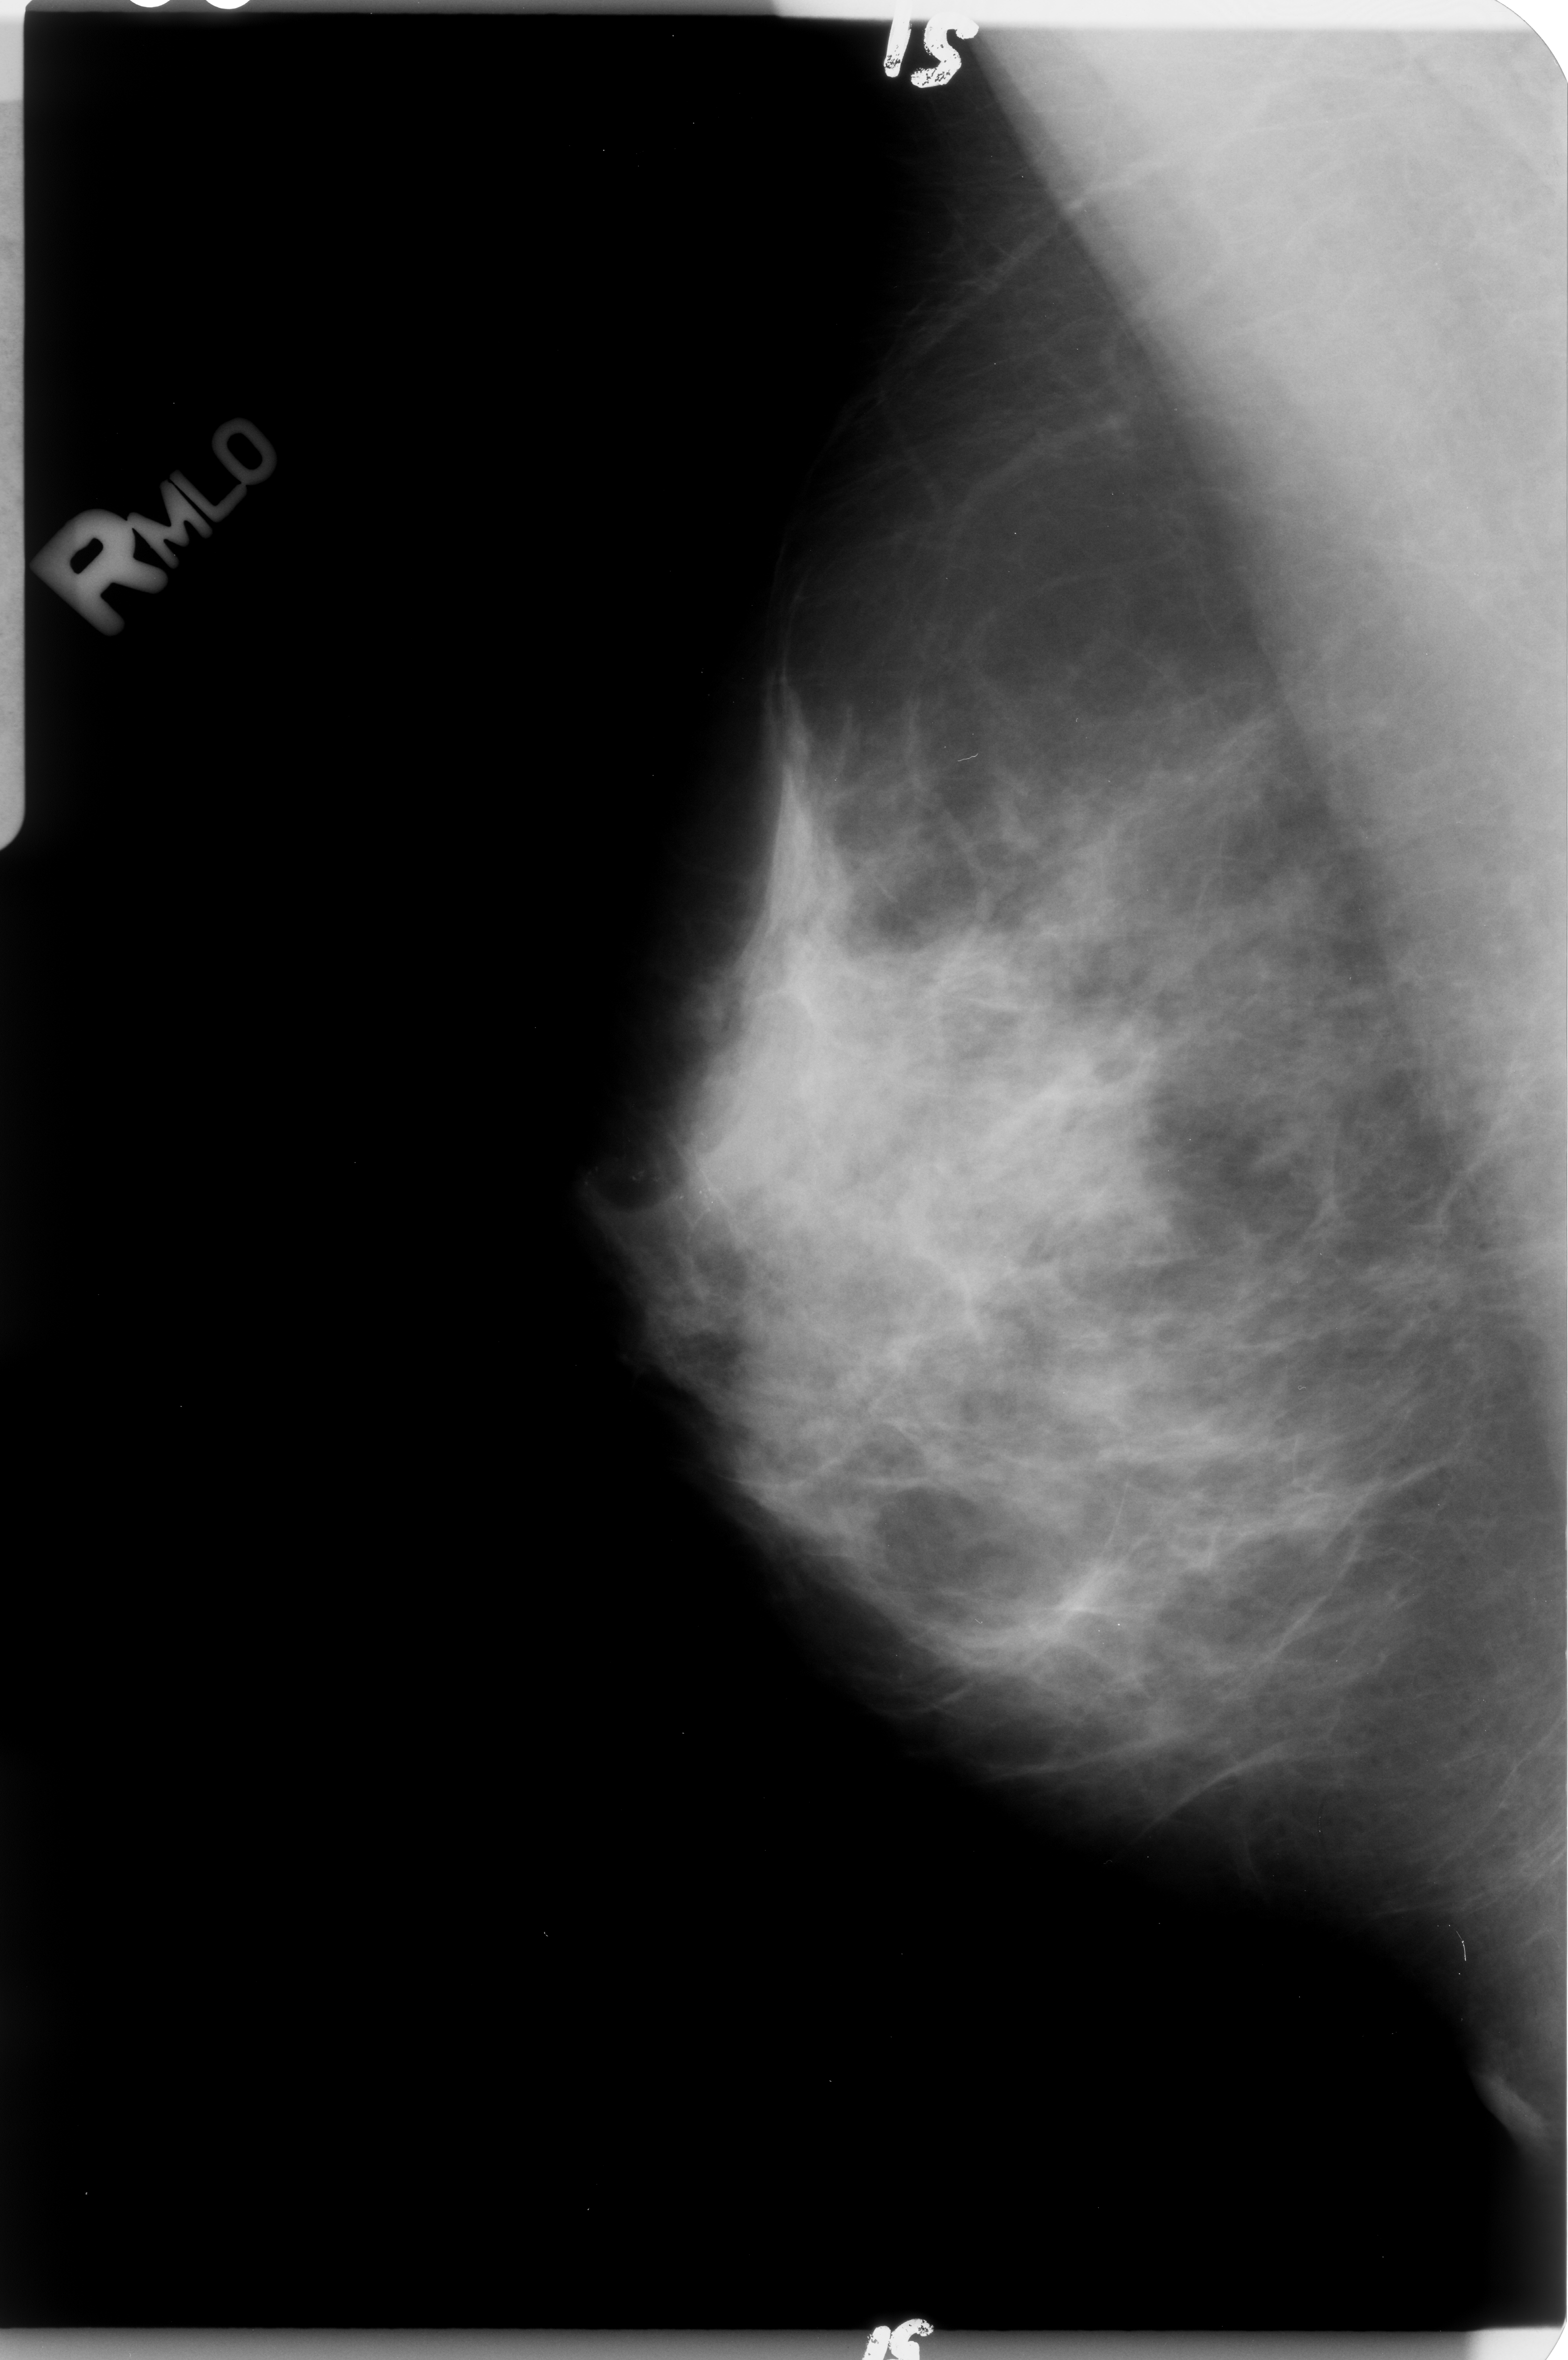
Digitized screen-film mammogram, right breast, MLO view, breast composition: heterogeneously dense (BI-RADS density category 3 of 4).
- Marked findings (only marked abnormalities are described; nothing is implied about the rest of the image): calcifications, morphology pleomorphic, distribution linear; BI-RADS assessment category 4; pathology result (as recorded, not read from the image): malignant.